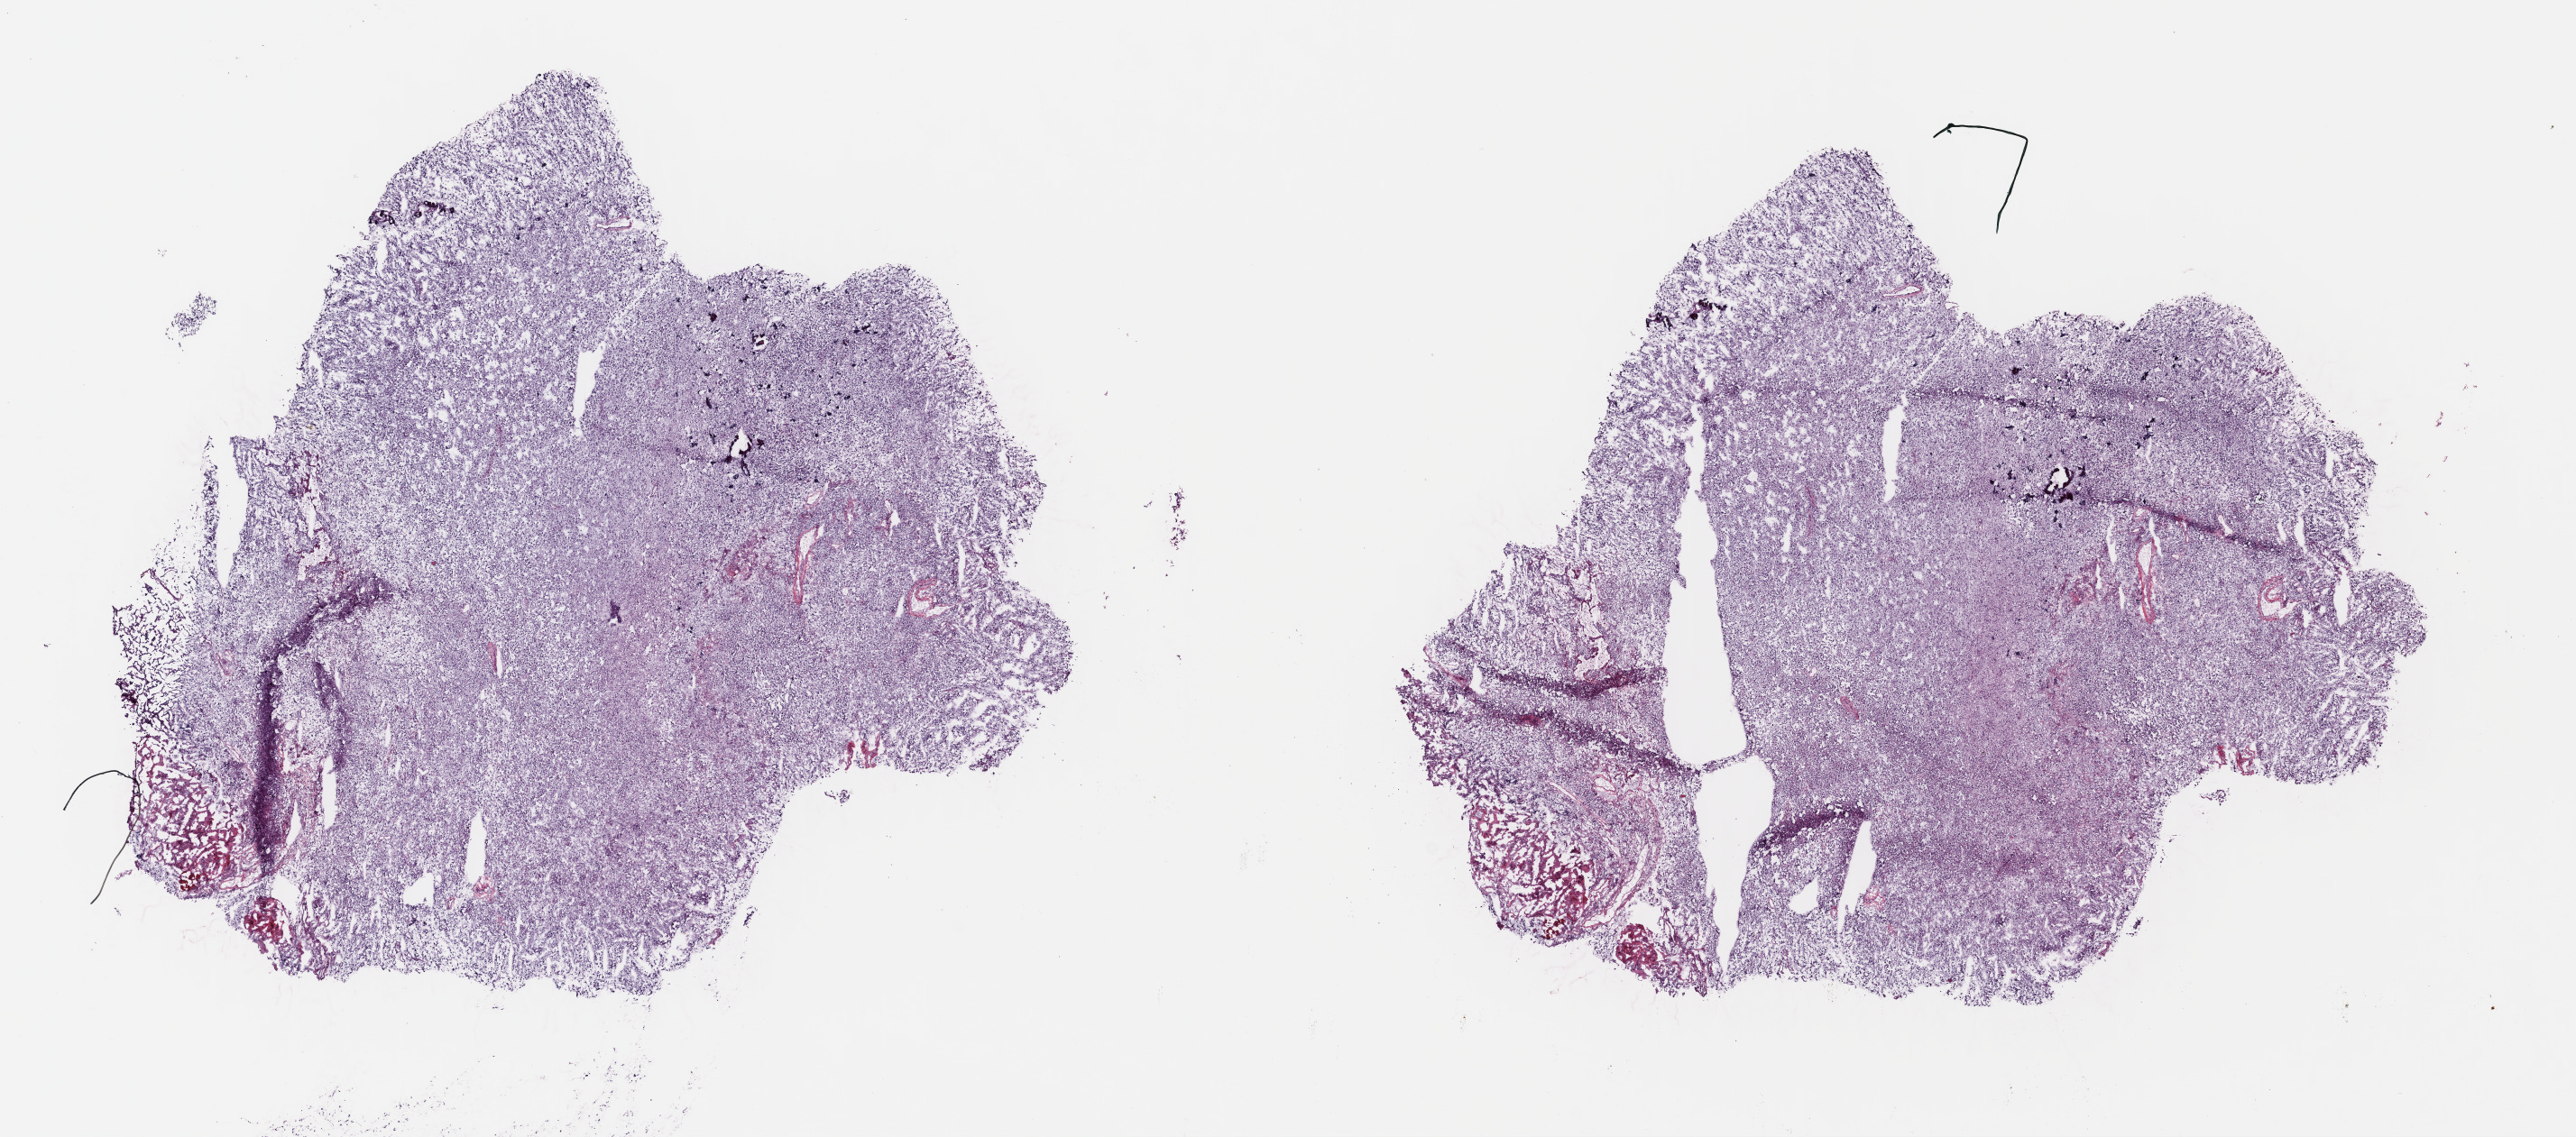
H&E-stained whole-slide image — a low-resolution overview of the entire scanned area, about 22.4 x 9.9 mm (acquisition: 40x scan). Frozen section from the top of the tissue portion. Sample: primary tumour, brain. Male patient; age at initial diagnosis 40 years. Histologic grade: G3 (poorly differentiated). Slide review estimates, as recorded: tumour cells 80%, tumour nuclei 90%, normal cells 10%, stromal cells 10%, necrosis 0%. Inflammatory infiltration, as recorded: lymphocyte infiltration 0%, monocyte infiltration 0%, neutrophil infiltration 0%.
Laterality: left. Pathologic diagnosis: Oligodendroglioma, anaplastic (cerebrum).